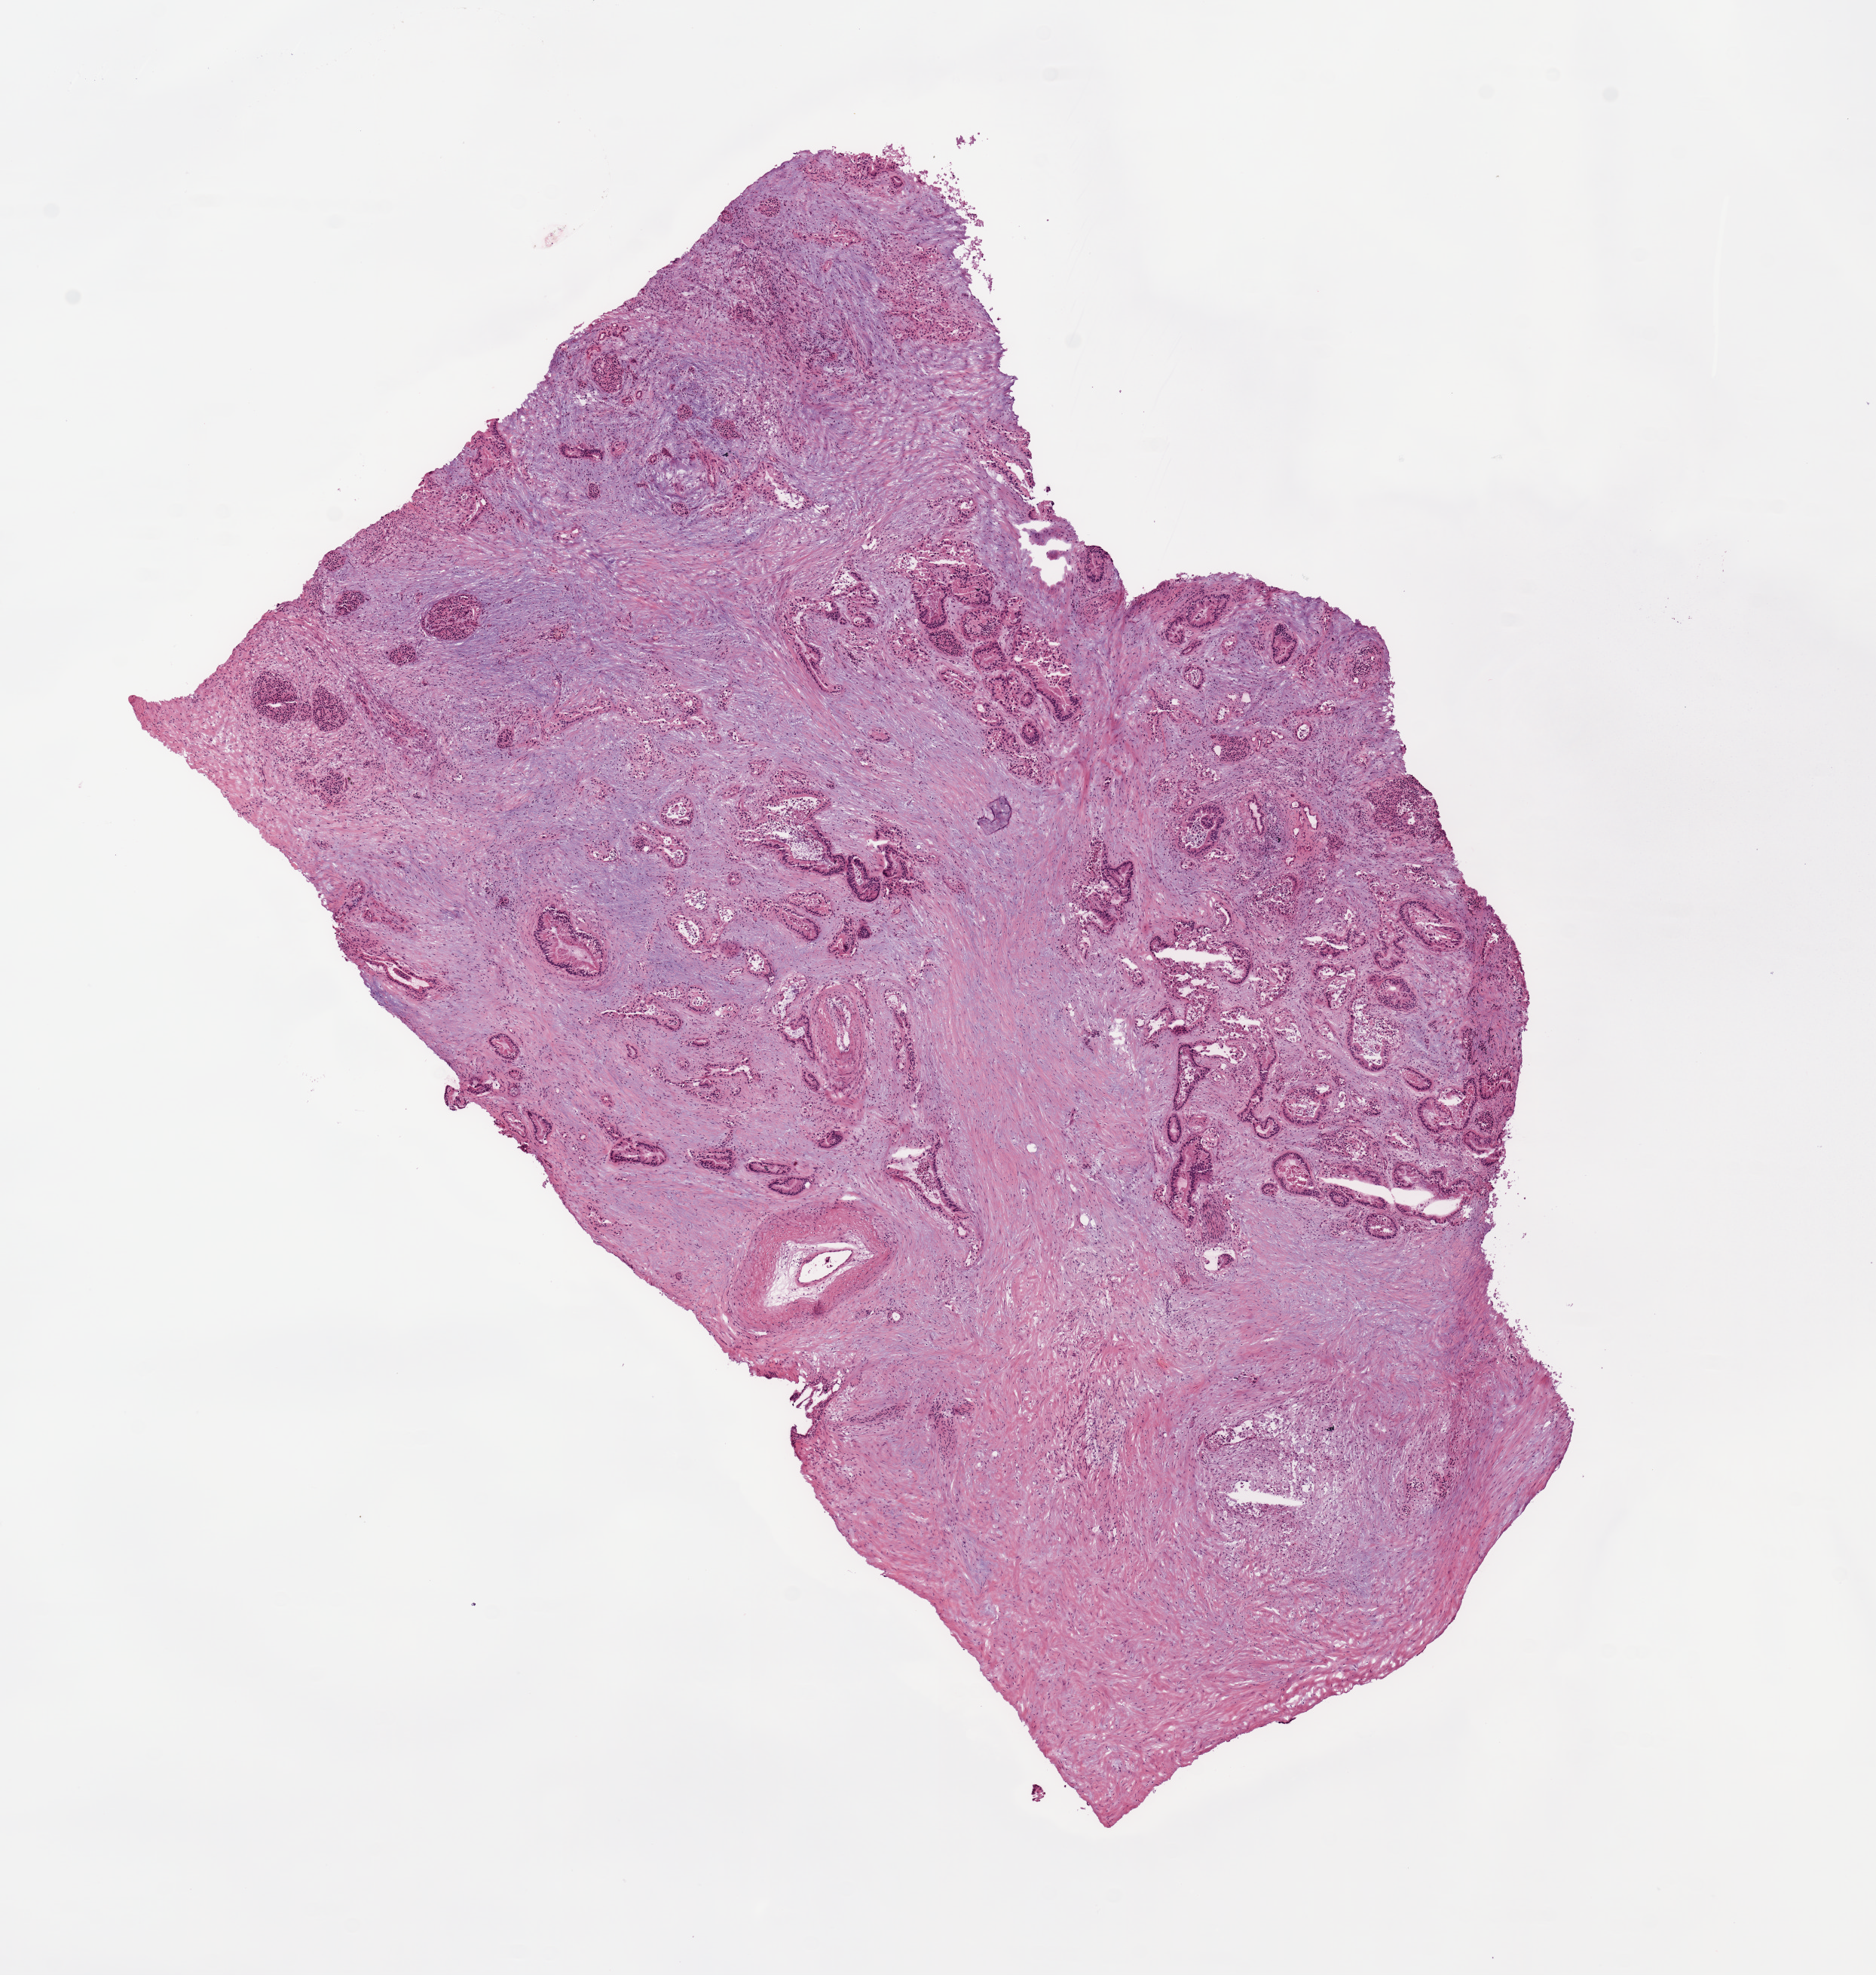
H&E-stained whole-slide image, shown as a low-resolution overview of the whole scanned area (about 9.8 x 10.4 mm), tumour tissue sample, pancreas. 69-year-old male patient. Histologic grade: G2 (moderately differentiated).
• diagnosis: Infiltrating duct carcinoma, NOS
• AJCC pathologic stage: IIA
• primary tumour site (as recorded): head